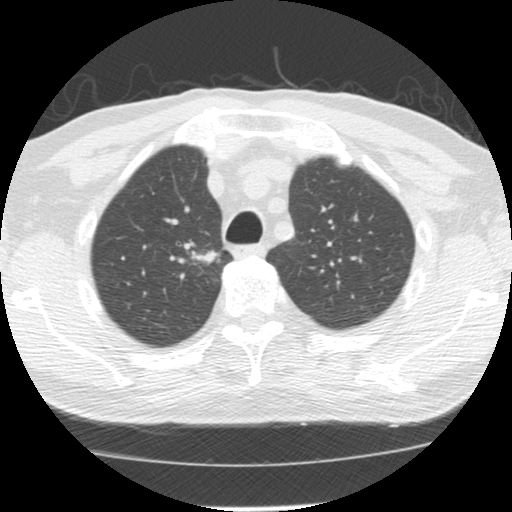
Low-dose screening chest CT, one axial slice; slice 106 of 139 in the series (ordered by position); reconstruction kernel STANDARD; 120 kVp; lung window (W 1500 / L -600 HU); 512 × 512 image matrix, field of view 310 × 310 mm.
Outlined on this slice (expert manual segmentation):
- lesion 1 (tumor, upper lobe of right lung): box from (x=191, y=250) to (x=219, y=265) px